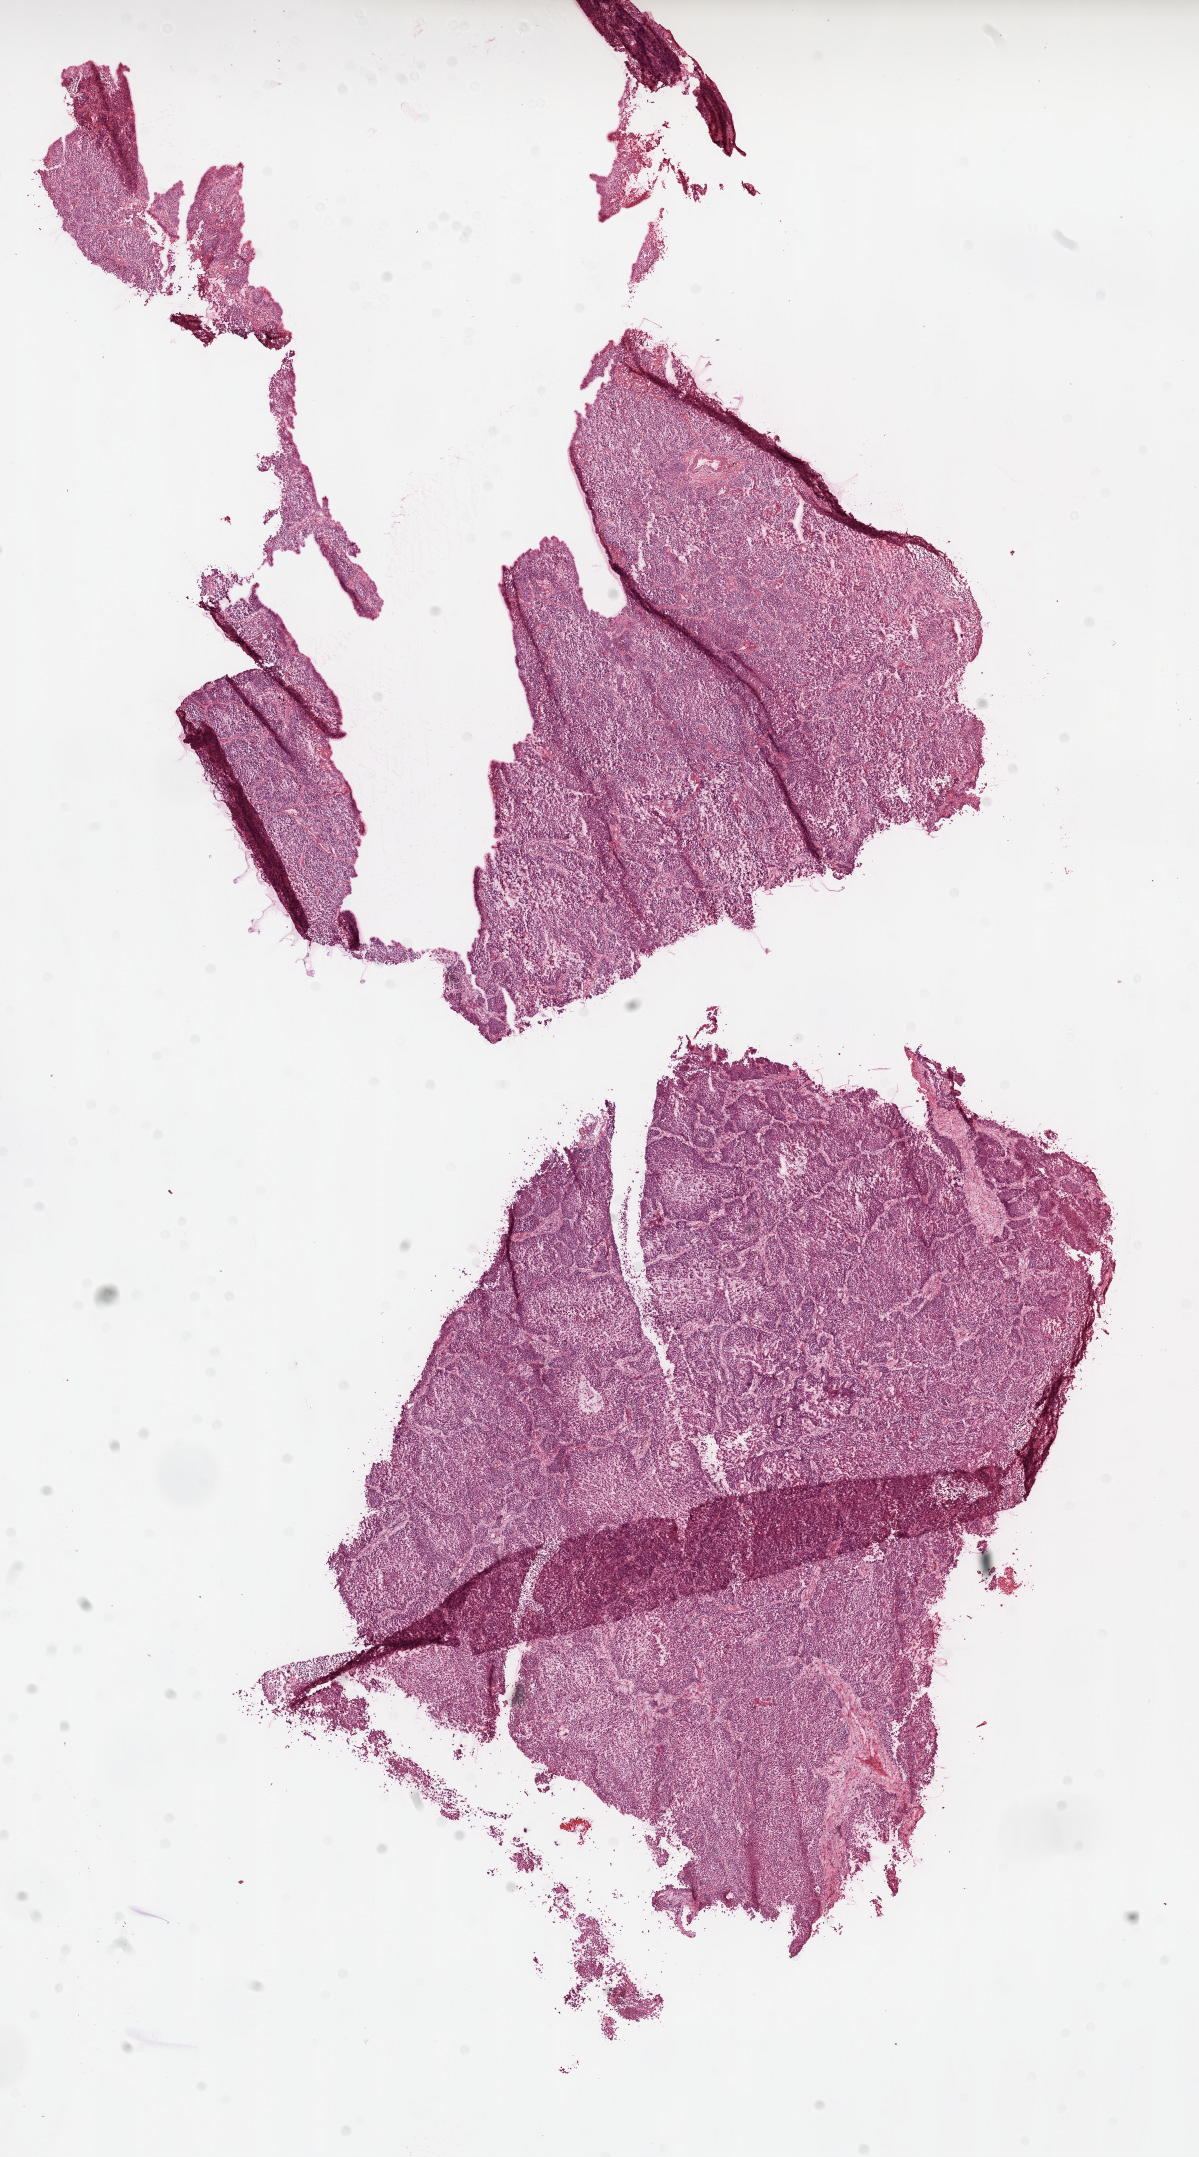
Digitized H&E tissue section (whole slide) — whole scanned area (about 9.7 x 17.4 mm, slide scanned at 20x) shown as a low-resolution overview, frozen section from the top of the tissue portion, sample: primary tumour, lung. Male, age 77 years at initial diagnosis. Slide review estimates, as recorded: tumour nuclei 95%, necrosis 0%.
Pathologic diagnosis: Squamous cell carcinoma, NOS (lower lobe, lung). Laterality: right. AJCC pathologic stage: IB. TNM: T2 N0 M0.